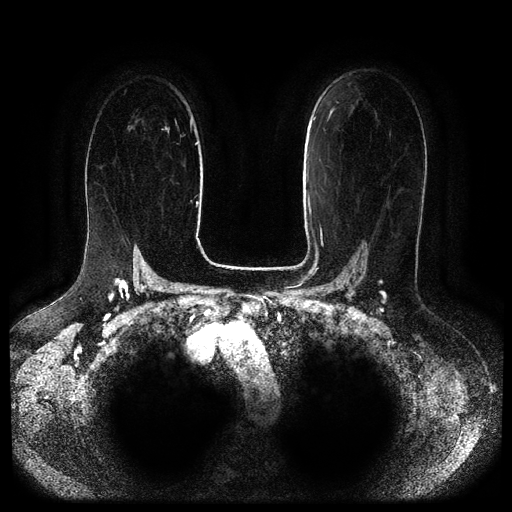
Breast MRI (dynamic contrast-enhanced, multi-phase), one axial slice; position 65 of 116 along the scan axis; dynamic contrast-enhanced series, time point 2 of 5 at this slice position (early post-contrast); 1.5 T; TE 2.6 ms, TR 5.3 ms; 2.1 mm slice thickness; 512 × 512 image matrix. Patient: female, 65 years.
Outlined on this slice (semi-automatic segmentation, software-assisted and operator-edited):
- breast lesion (labelled benign in the annotation): bounding box (x1, y1, x2, y2) in pixels: (161, 126, 170, 133)